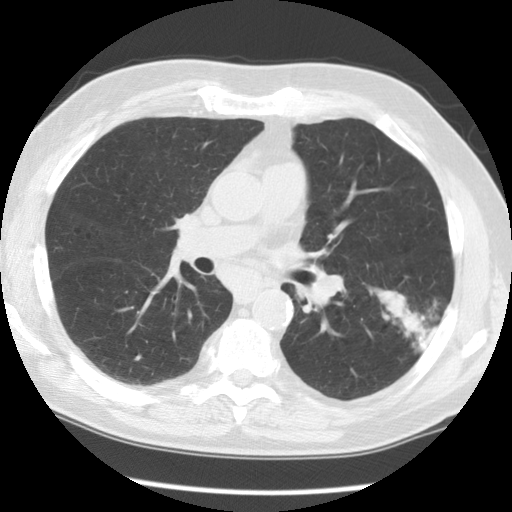
Low-dose screening chest CT, one axial slice. 120 kVp. Lung window (W 1500 / L -600 HU). 512 × 512 image matrix, field of view 340 × 340 mm.
Structures marked on this image (expert manual segmentation):
- lesion 1 (tumor, lower lobe of left lung): bounding box (x1, y1, x2, y2) in pixels: (374, 289, 437, 352)